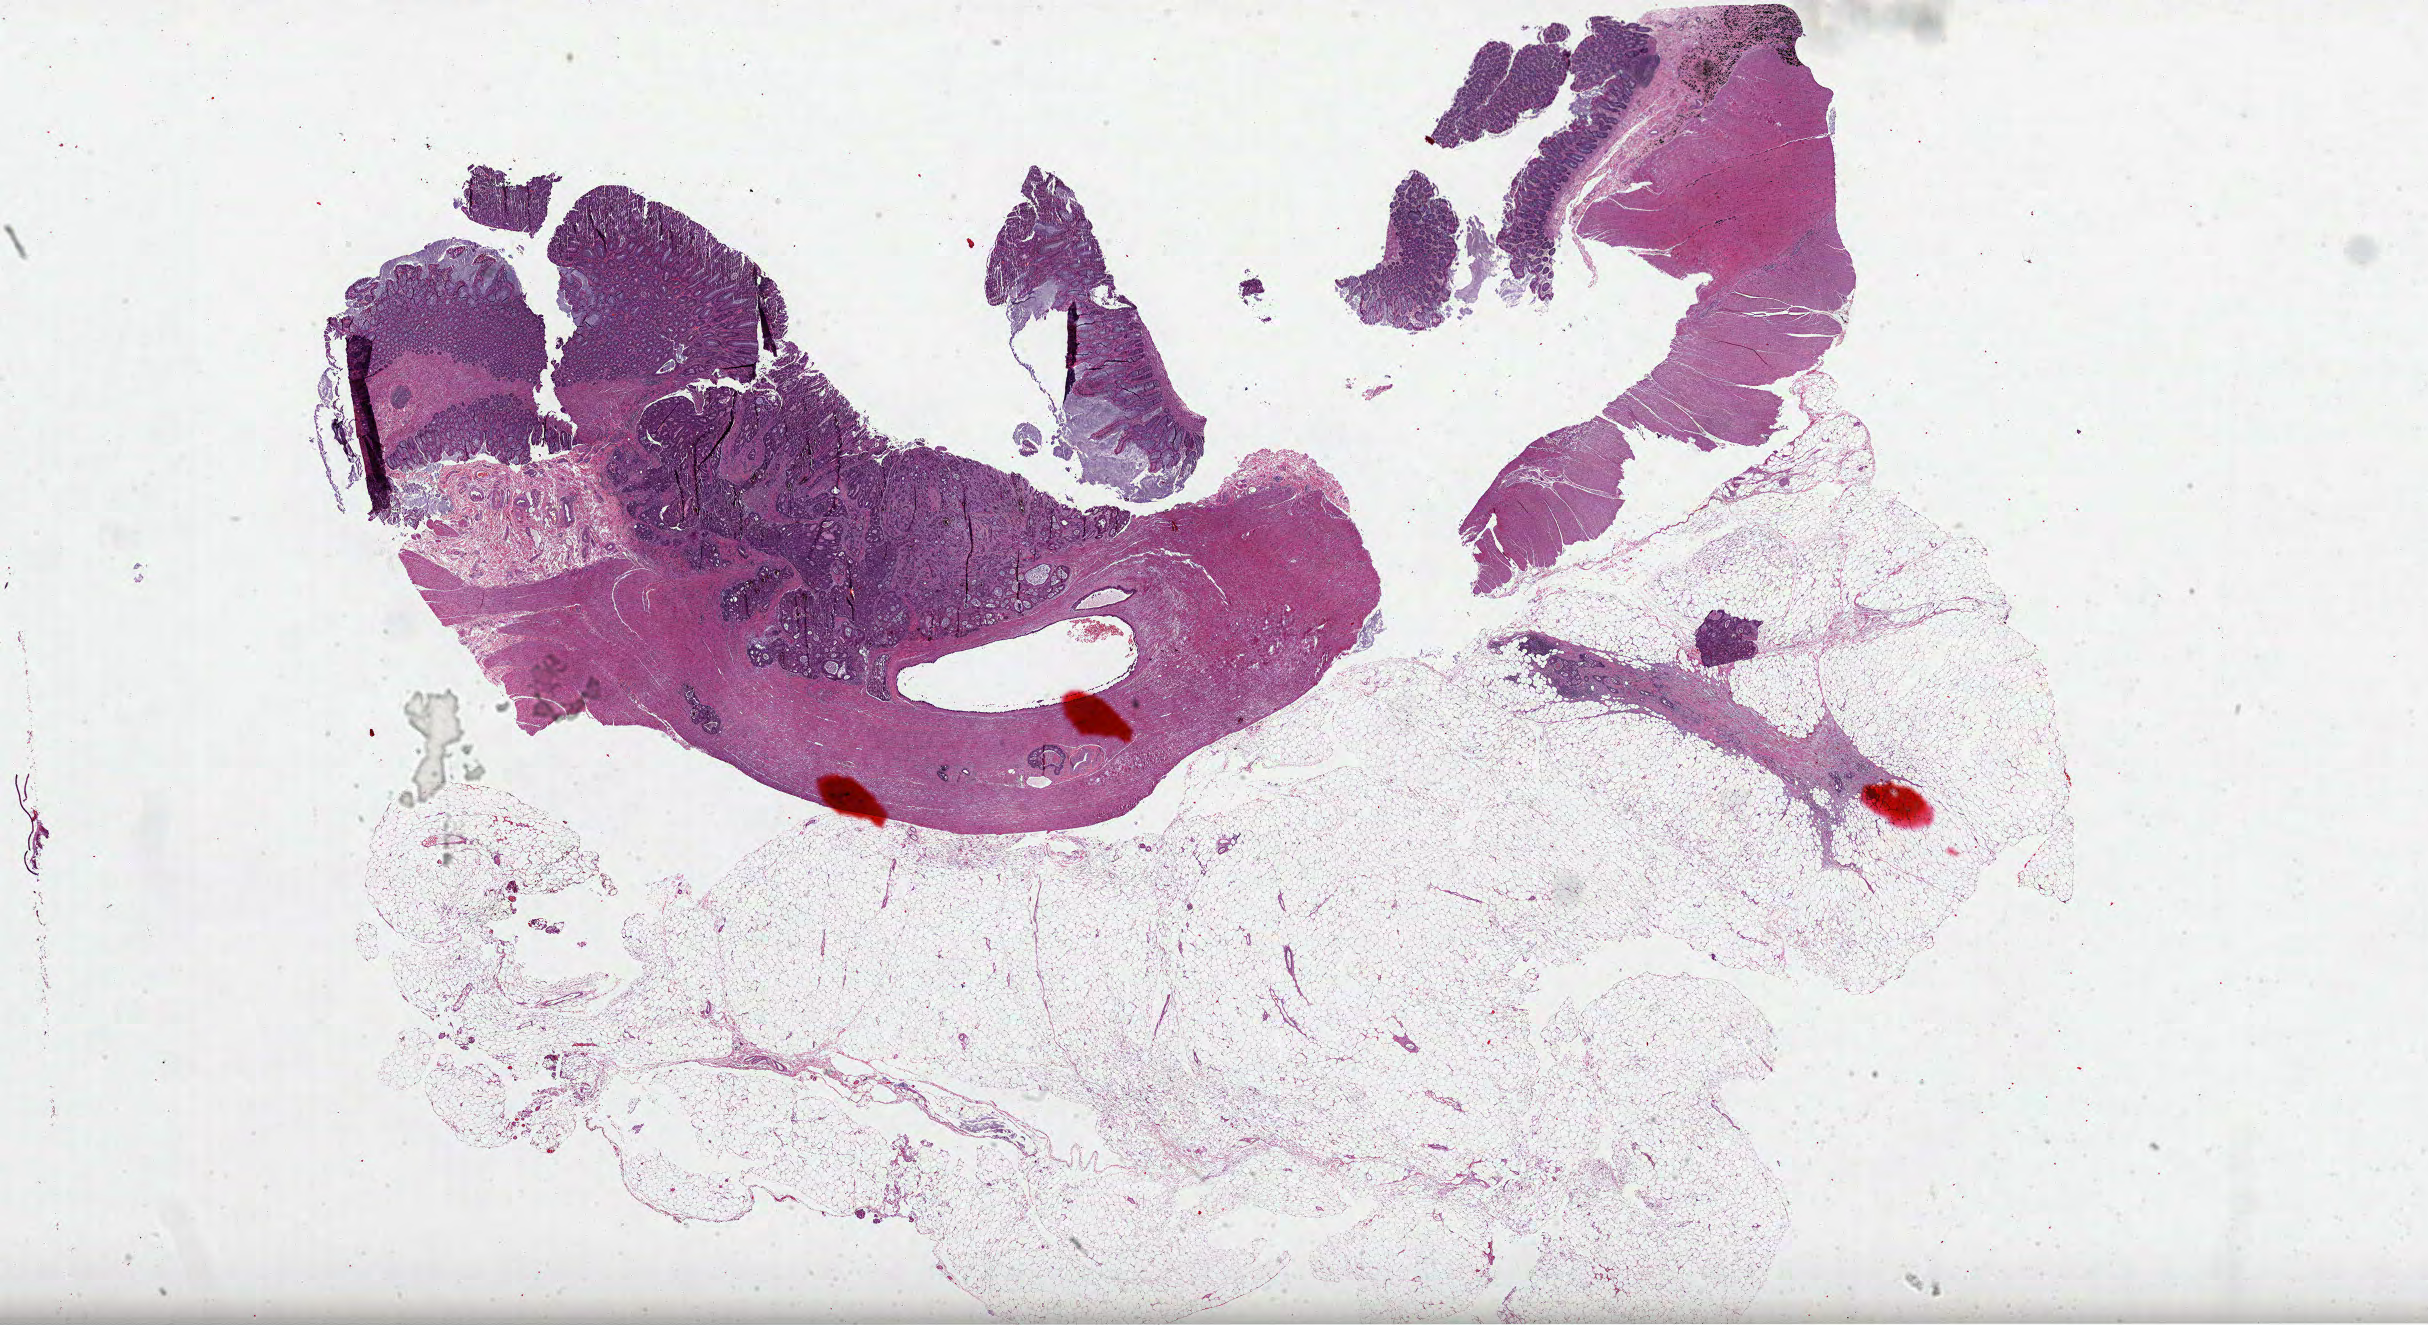
Whole-slide histology image, Hematoxylin and eosin (H&E) stained, a low-resolution overview of the entire scanned area, about 39.2 x 21.4 mm (acquisition: 40x scan), formalin-fixed paraffin-embedded (FFPE) diagnostic section, colon, primary tumour sample. Female patient; age at initial diagnosis 70 years.
• pathologic diagnosis: Adenocarcinoma, NOS (sigmoid colon)
• lymph nodes positive (case pathology): 1 of 17 examined
• AJCC pathologic stage: IIIB